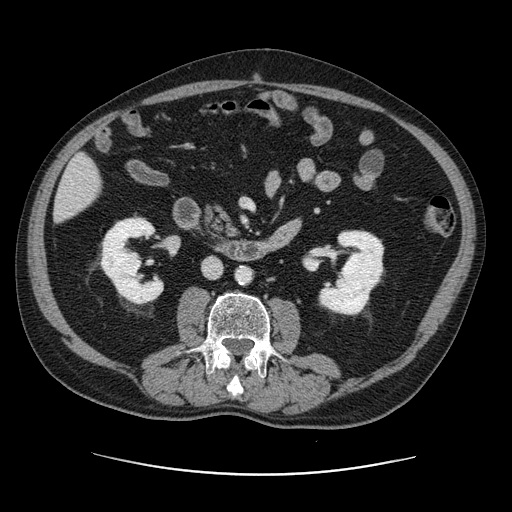
Contrast-enhanced abdominal CT, one axial slice. Position 34 of 141 along the scan axis. 120 kVp. Intravenous contrast given. Soft-tissue window (W 400 / L 40 HU). 512 × 512 image matrix, field of view 395 × 395 mm. Male patient, age 72 years. Case-level facts recorded for this patient, not image findings: diagnosis: colorectal cancer liver metastases, imaged before liver resection; multiple liver metastases: yes; largest metastasis: 5.4 cm; disease in both lobes: yes.
Structures marked on this image (manually delineated by an expert):
- liver: box from (x=55, y=156) to (x=102, y=221) px
- planned liver remnant (the part of the liver to remain after resection): (x=55, y=156)–(x=102, y=221)